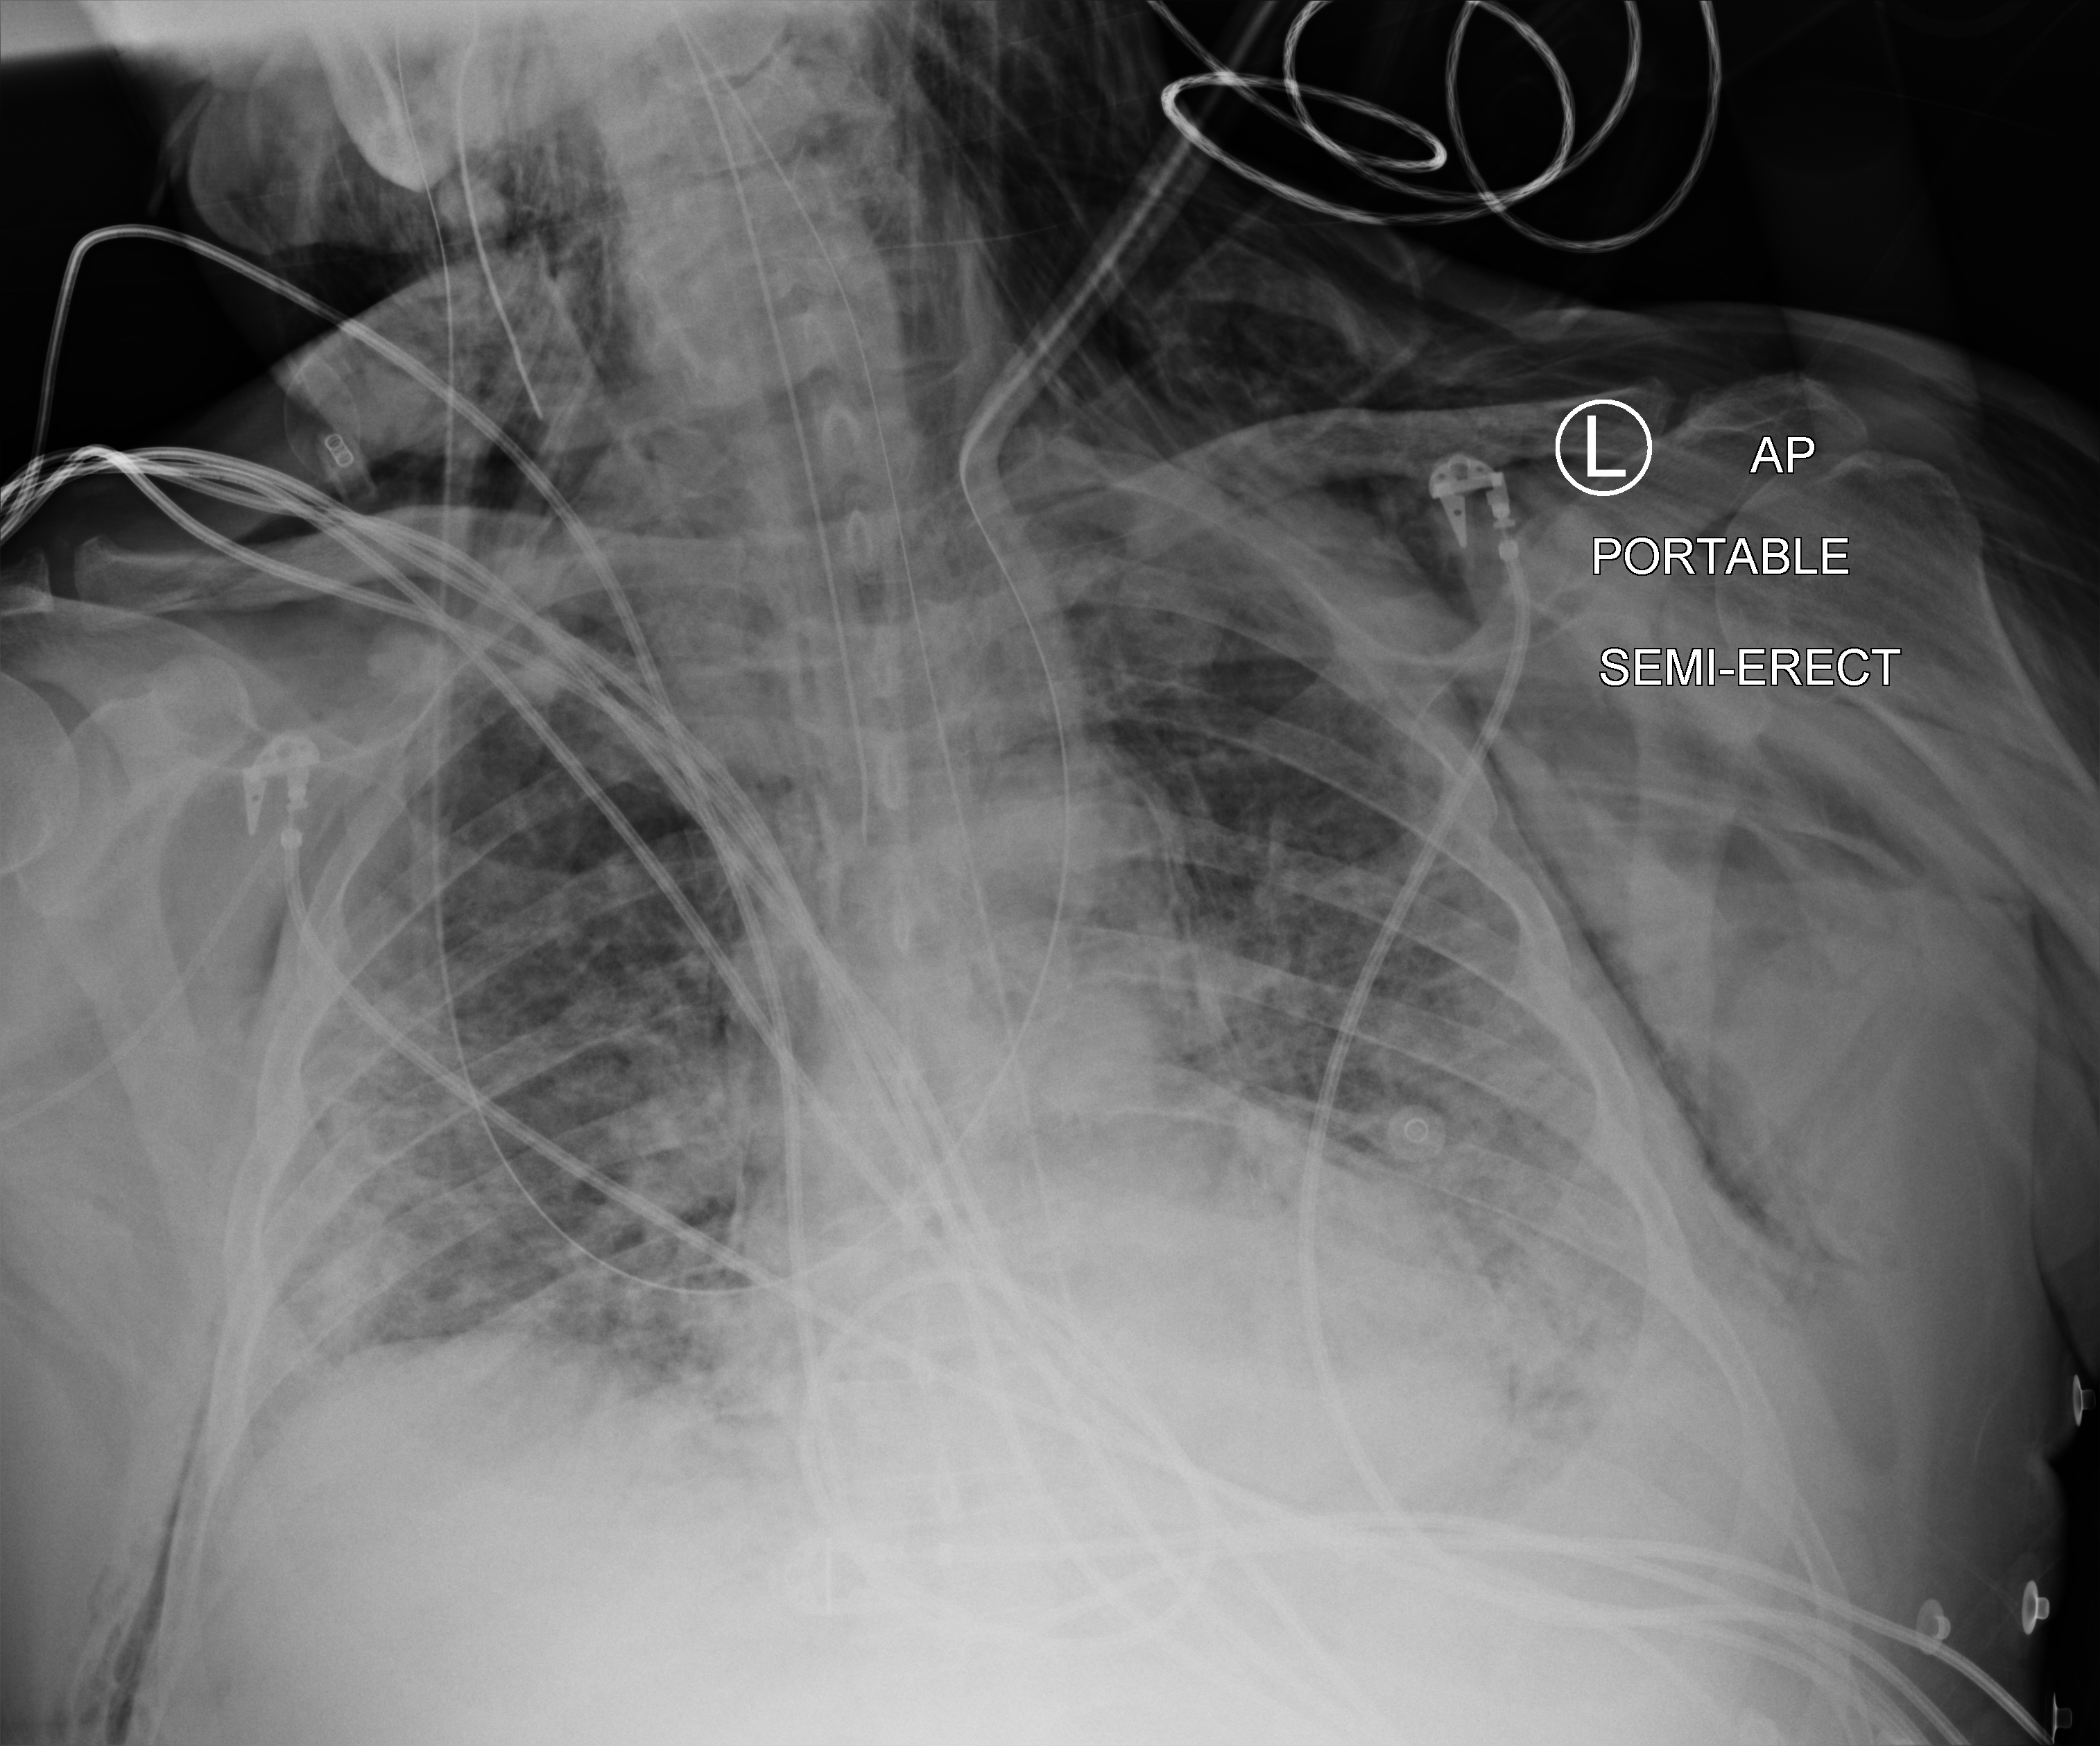
Bedside chest radiograph (computed radiography); anteroposterior (AP) projection. Patient hospitalised with COVID-19; male, aged 60–74 years.
Admission-level facts for this patient (not findings on this image; timing relative to this image not recorded): length of hospital stay: 26 days; diabetes (admission record): yes; other chronic lung disease (admission record): no.